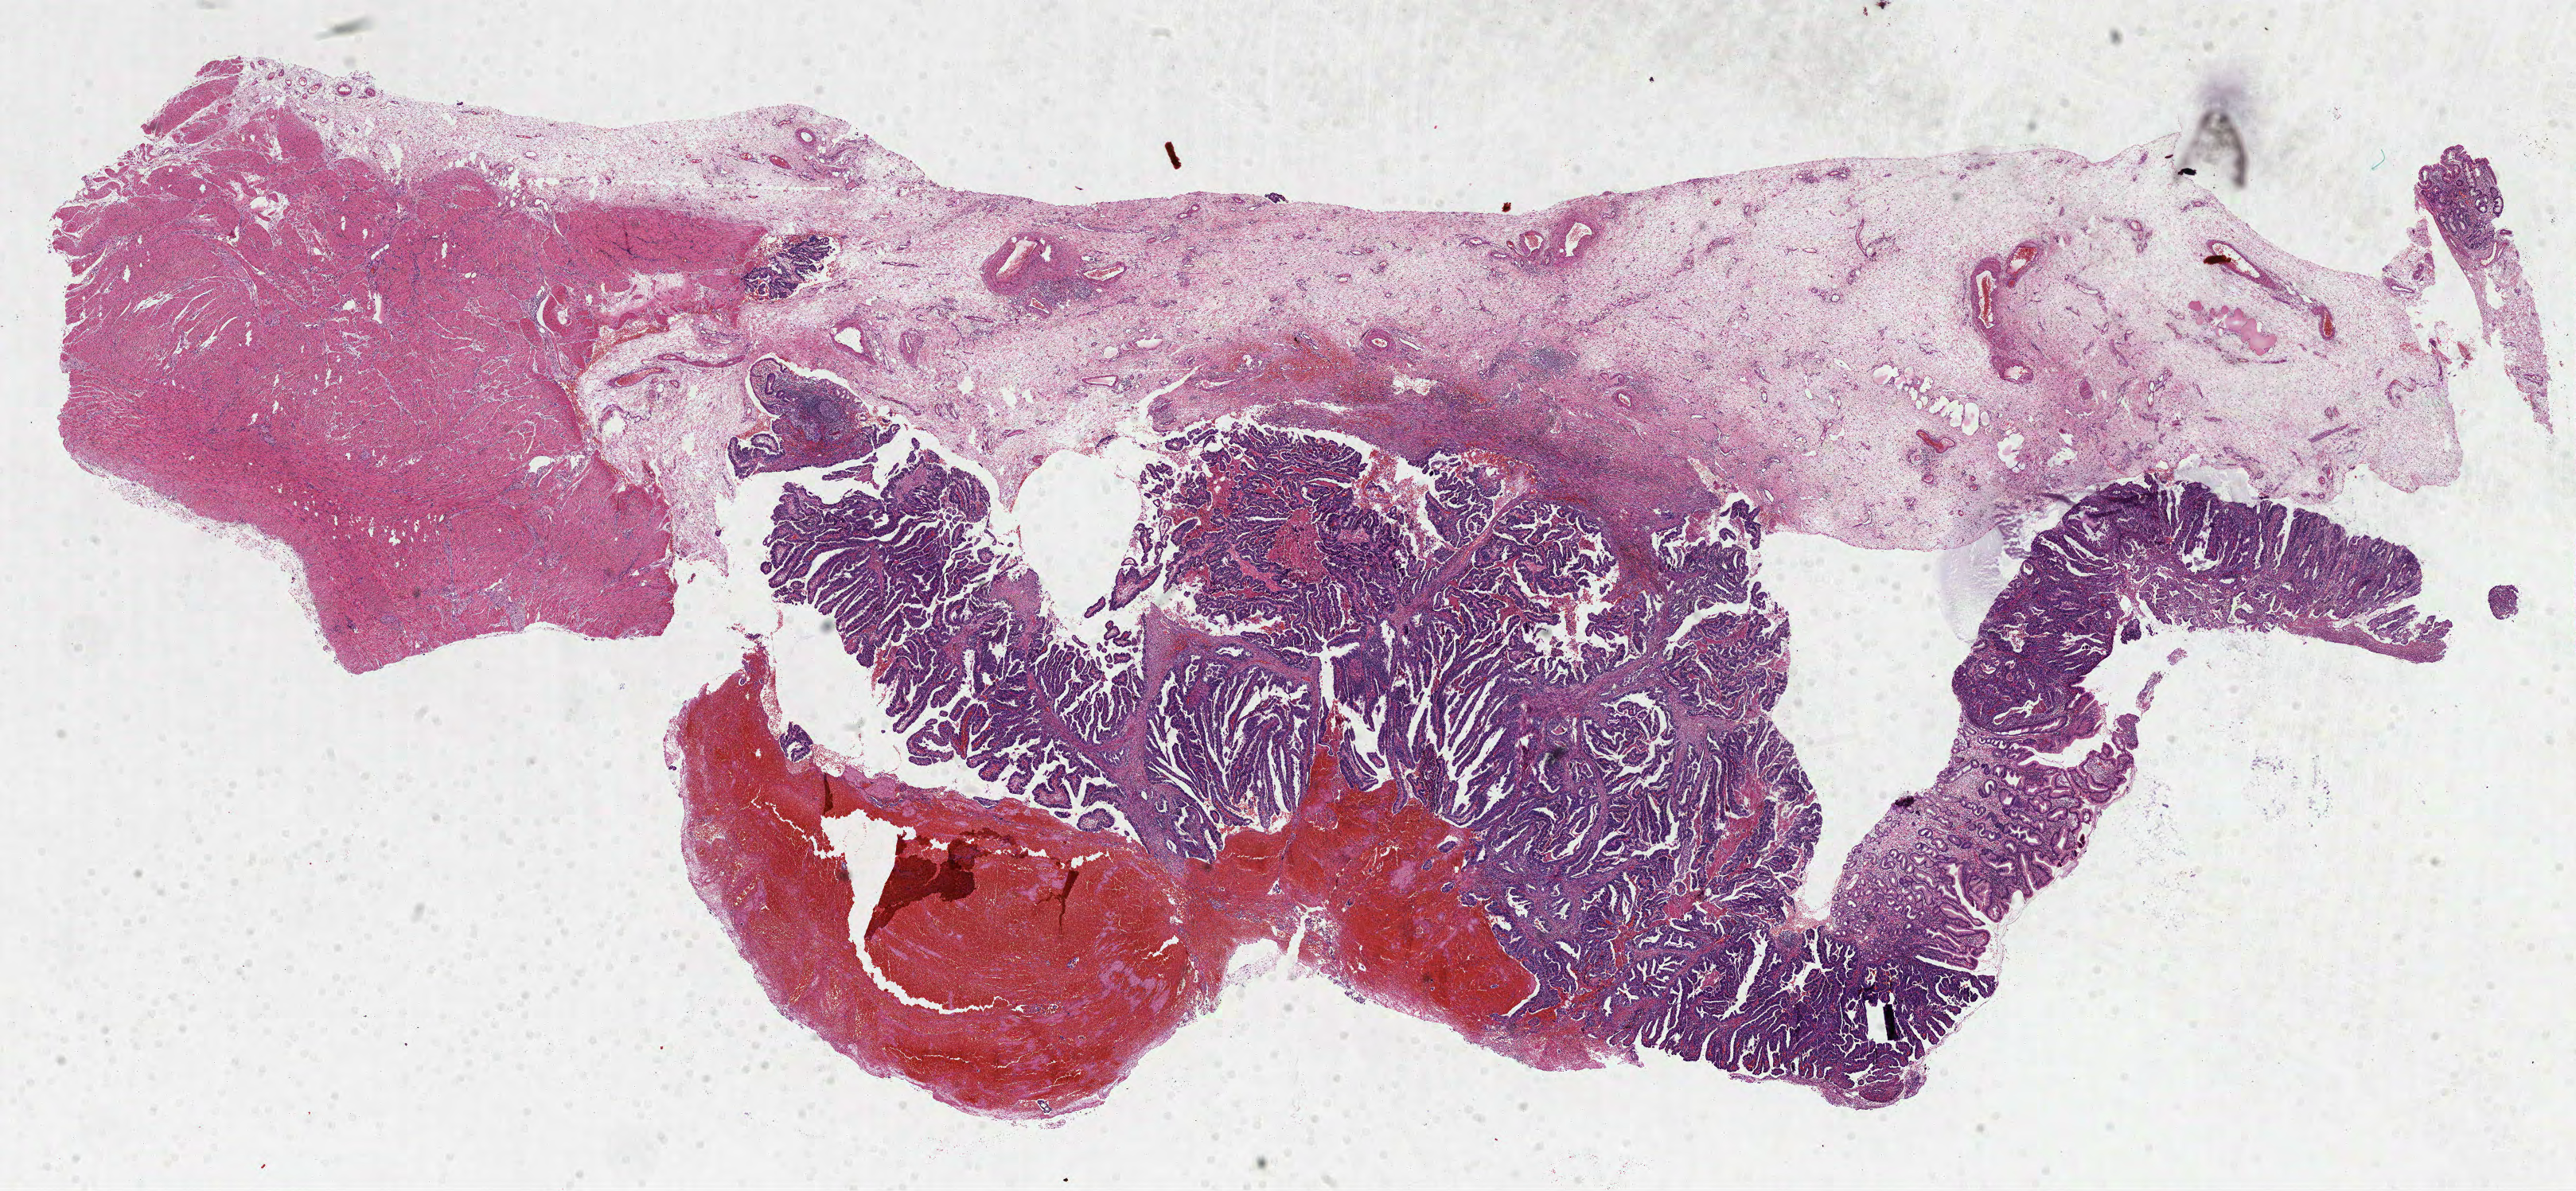
Digitized H&E tissue section (whole slide), low-resolution overview of the scanned area, about 26.1 x 12.1 mm (acquisition: 40x scan). FFPE section. Stomach, primary tumour sample. Patient: female, age at initial diagnosis 51 years. Histologic grade: G1 (well differentiated).
- histologic diagnosis: Papillary adenocarcinoma, NOS (gastric antrum)
- AJCC pathologic stage: II